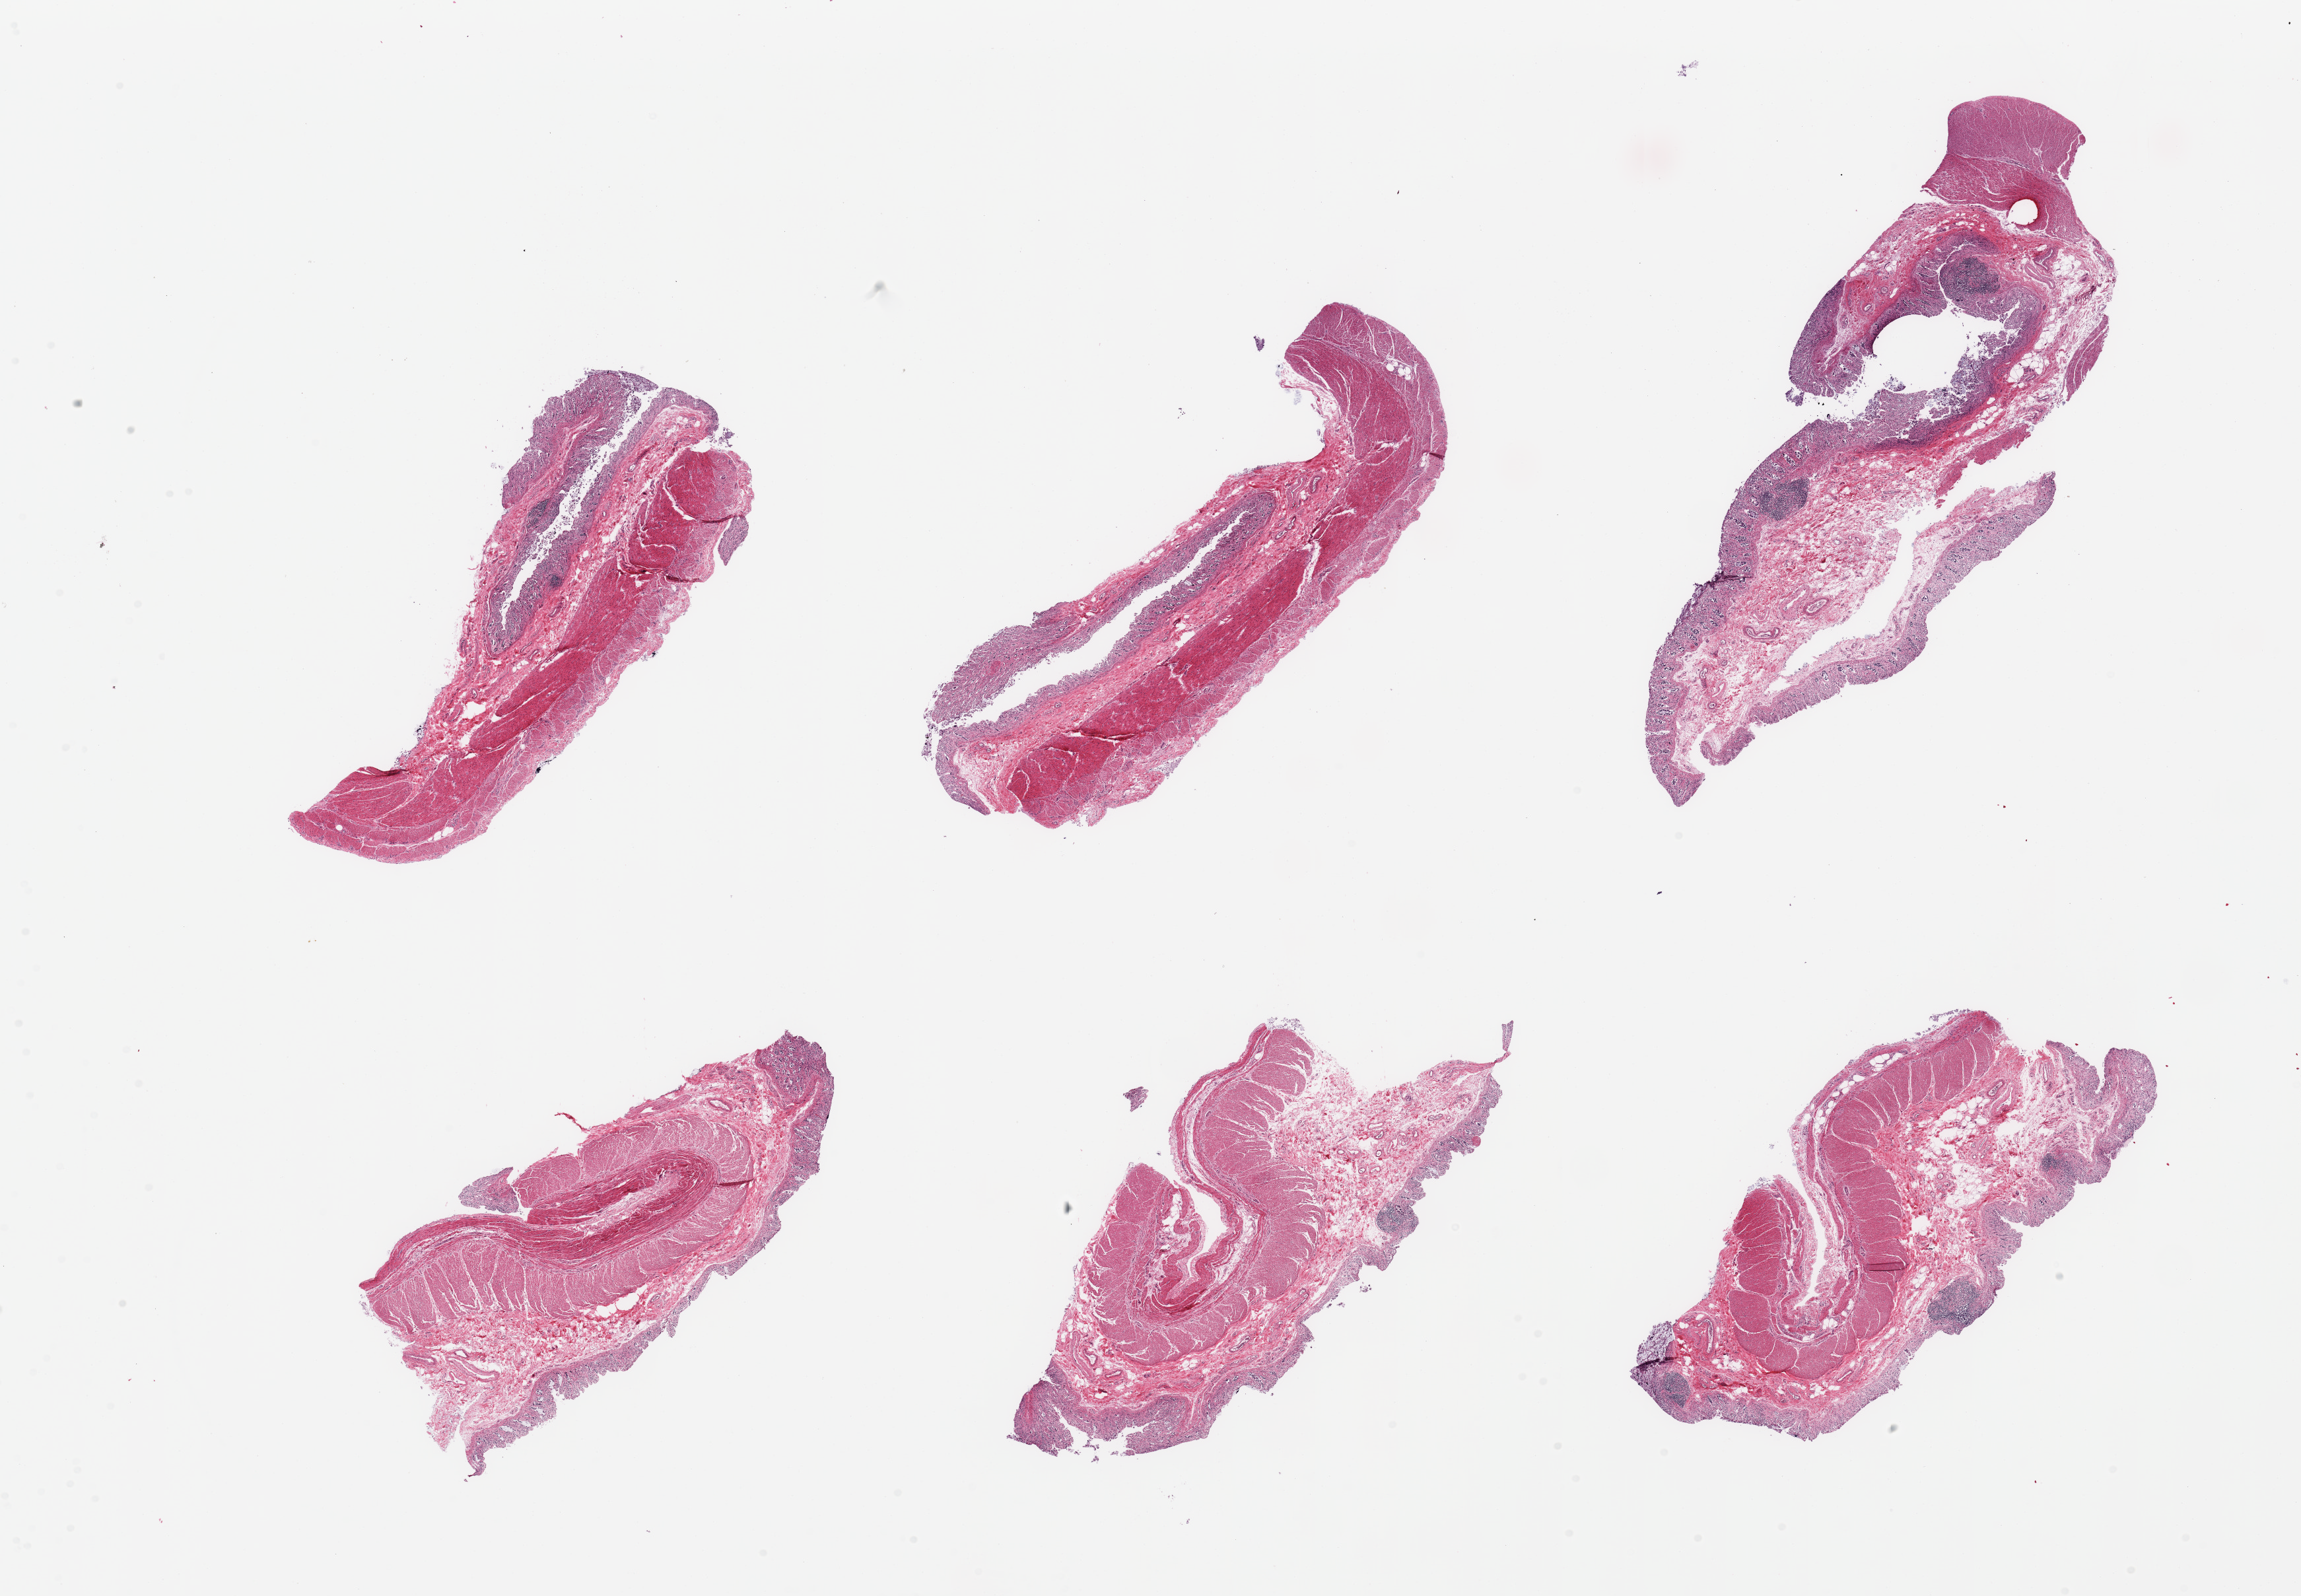
Digitized hematoxylin and eosin (H&E)-stained section, whole scanned area (about 27.6 x 19.1 mm, acquisition: 20x scan) shown as a low-resolution overview; PAXgene-fixed, paraffin-embedded tissue; target tissue: transverse colon; tissue donor sample. Male donor.
Review note (as recorded): 6 pieces, target mucosa up to ~0.4mm, glandular elements totally autolyzed.